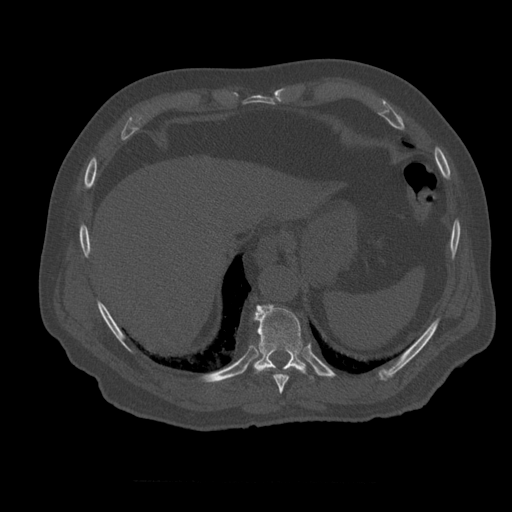
CT including the spine, one axial slice. Position 307 of 399 along the scan axis. 120 kVp. Bone window (W 1800 / L 400 HU). 1.25 mm slice thickness. 512 × 512 image matrix, field of view 407 × 407 mm. Patient age 73 years. From the clinical record (not read from this slice): primary cancer: prostate; vertebrae with lytic lesions (as recorded): L2.
Outlined on this slice (semi-automatic segmentation, software-assisted and operator-edited):
- T10 vertebra: bounding box (x1, y1, x2, y2) in pixels: (253, 304, 320, 381)
- T12 vertebra: (270, 350, 276, 357)
- T9 vertebra: (262, 367, 303, 394)